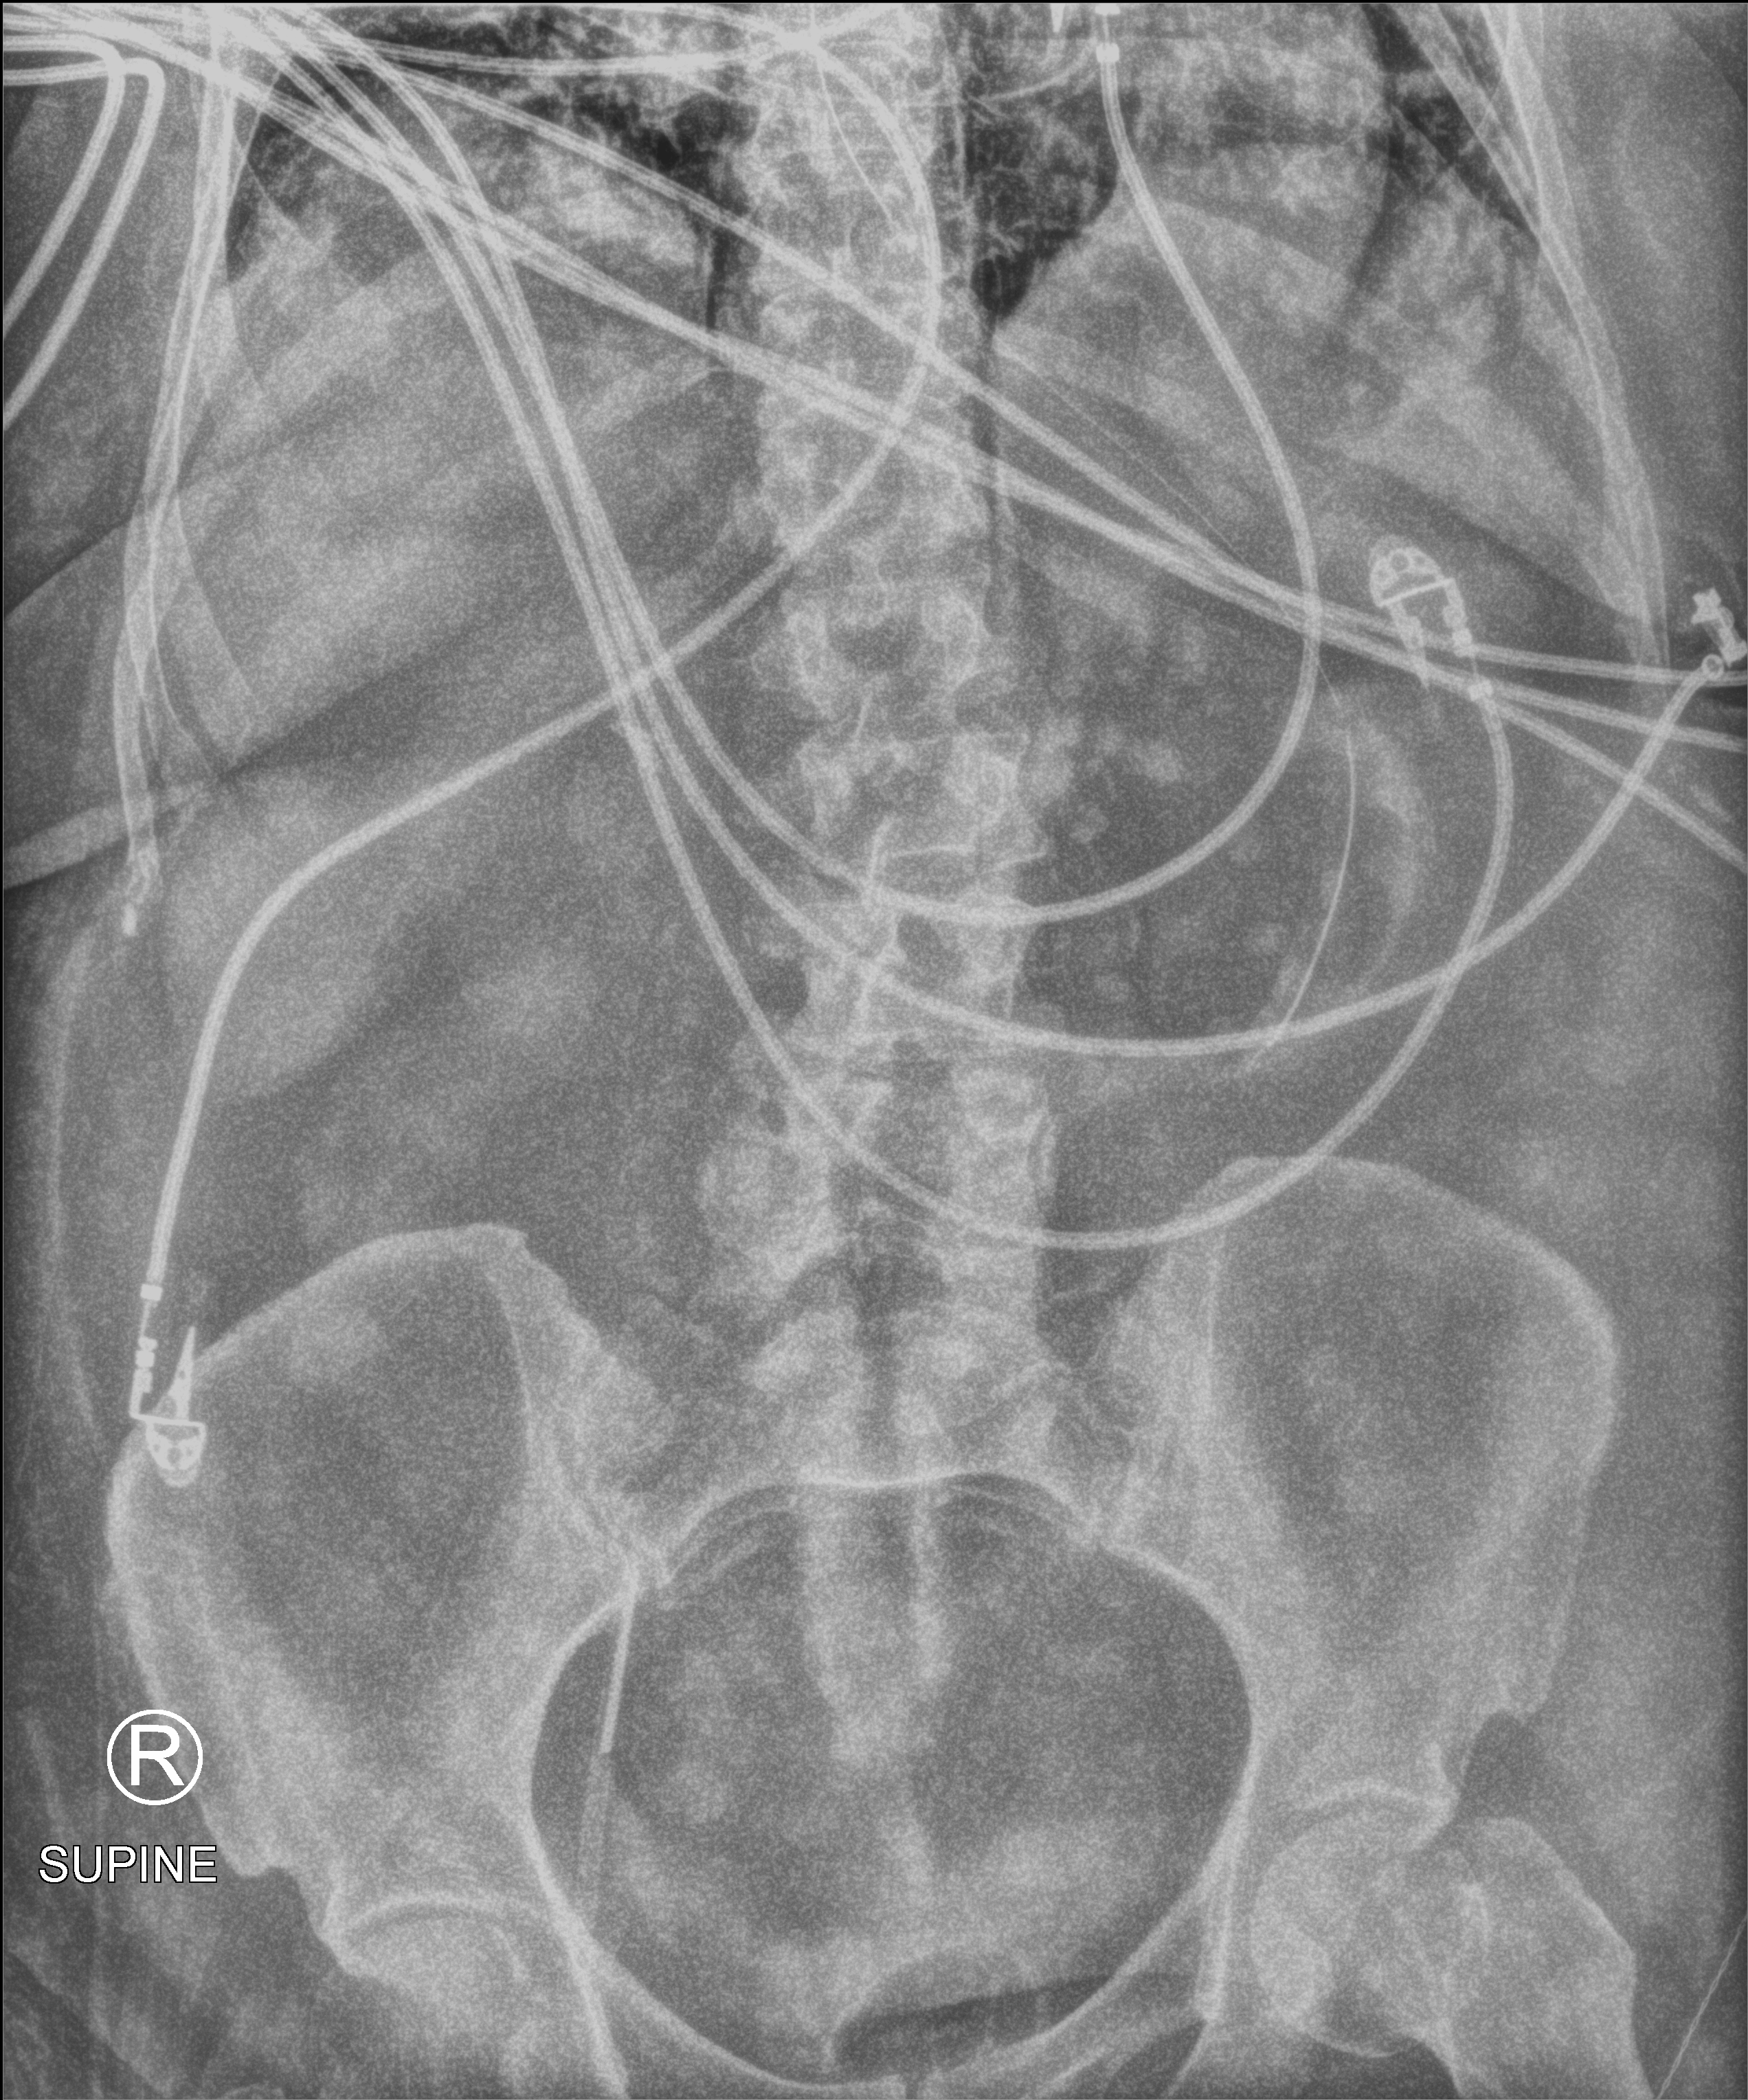
Abdomen X-ray (portable), anteroposterior (AP) projection. Patient hospitalised with COVID-19; female, aged 60–74 years.
From the hospital-stay record, not from the radiograph (when in the stay this image was taken is not recorded): mechanically ventilated during this hospital stay: yes.